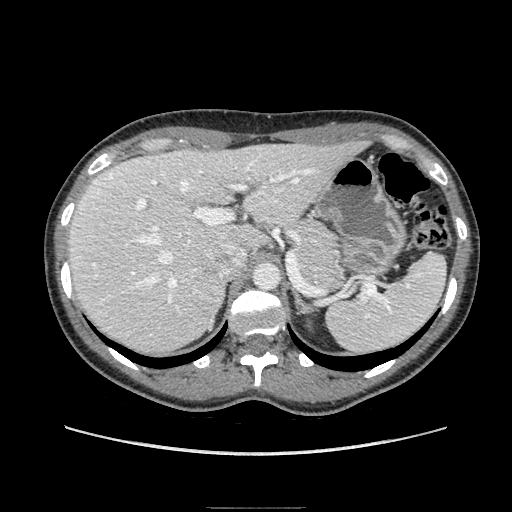
Contrast-enhanced abdominal CT, one axial slice. Position 126 of 193 along the scan axis. Soft-tissue window (W 400 / L 40 HU). 512 × 512 image matrix, field of view 380 × 380 mm. Female patient. Case-level facts recorded for this patient, not image findings: diagnosis: adrenocortical carcinoma; tumour side: right adrenal; tumour size at pathology: 3 cm; Ki-67 index: 4 %; stage (as recorded): 1.
Outlined on this slice (semi-automatically segmented with operator editing):
- mass: bounding box [x1, y1, x2, y2] px = [195, 276, 223, 328]